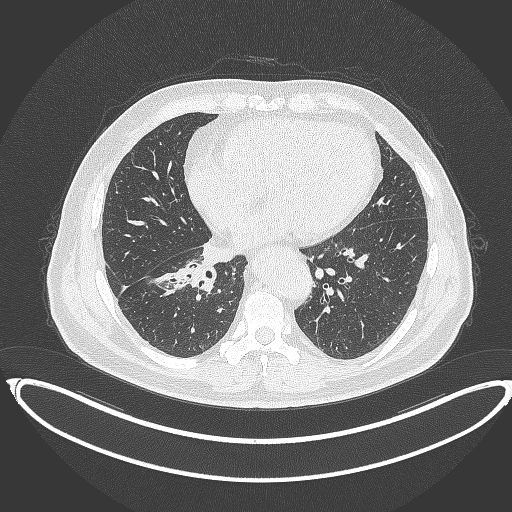
Chest CT, one axial slice; position 160 of 387 along the scan axis; reconstruction kernel B70f; lung window (W 1500 / L -600 HU); 512 × 512 image matrix, field of view 448 × 448 mm. Male patient, age 61 years. Case-level facts recorded for this patient, not image findings: clinical TNM (as recorded): T1b N1 M0.
Annotated regions visible in this slice (rectangle marked by the reading radiologist):
- lung tumour (recorded histology: squamous cell carcinoma): bounding box (x1, y1, x2, y2) in pixels: (175, 256, 219, 294)